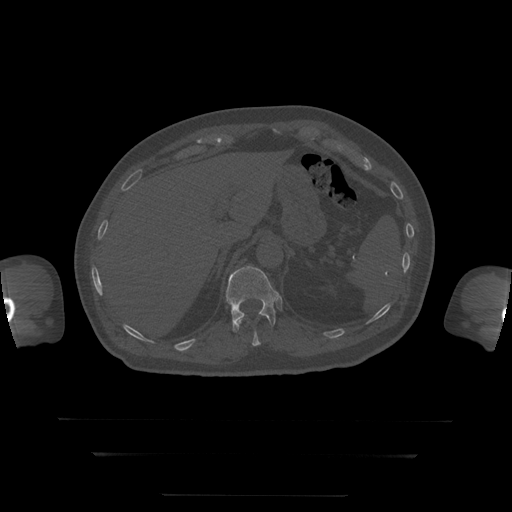
CT including the spine, one axial slice; slice 84 of 397 in the series (ordered by position); bone window (W 1800 / L 400 HU); 1.25 mm slice thickness; 512 × 512 image matrix. Patient age 73 years. From the clinical record (not read from this slice): primary cancer: prostate.
Structures marked on this image (semi-automatically segmented with operator editing):
- T11 vertebra: bounding box <238,317,275,347> (left, top, right, bottom; pixels)
- T12 vertebra: <226,266,281,333>